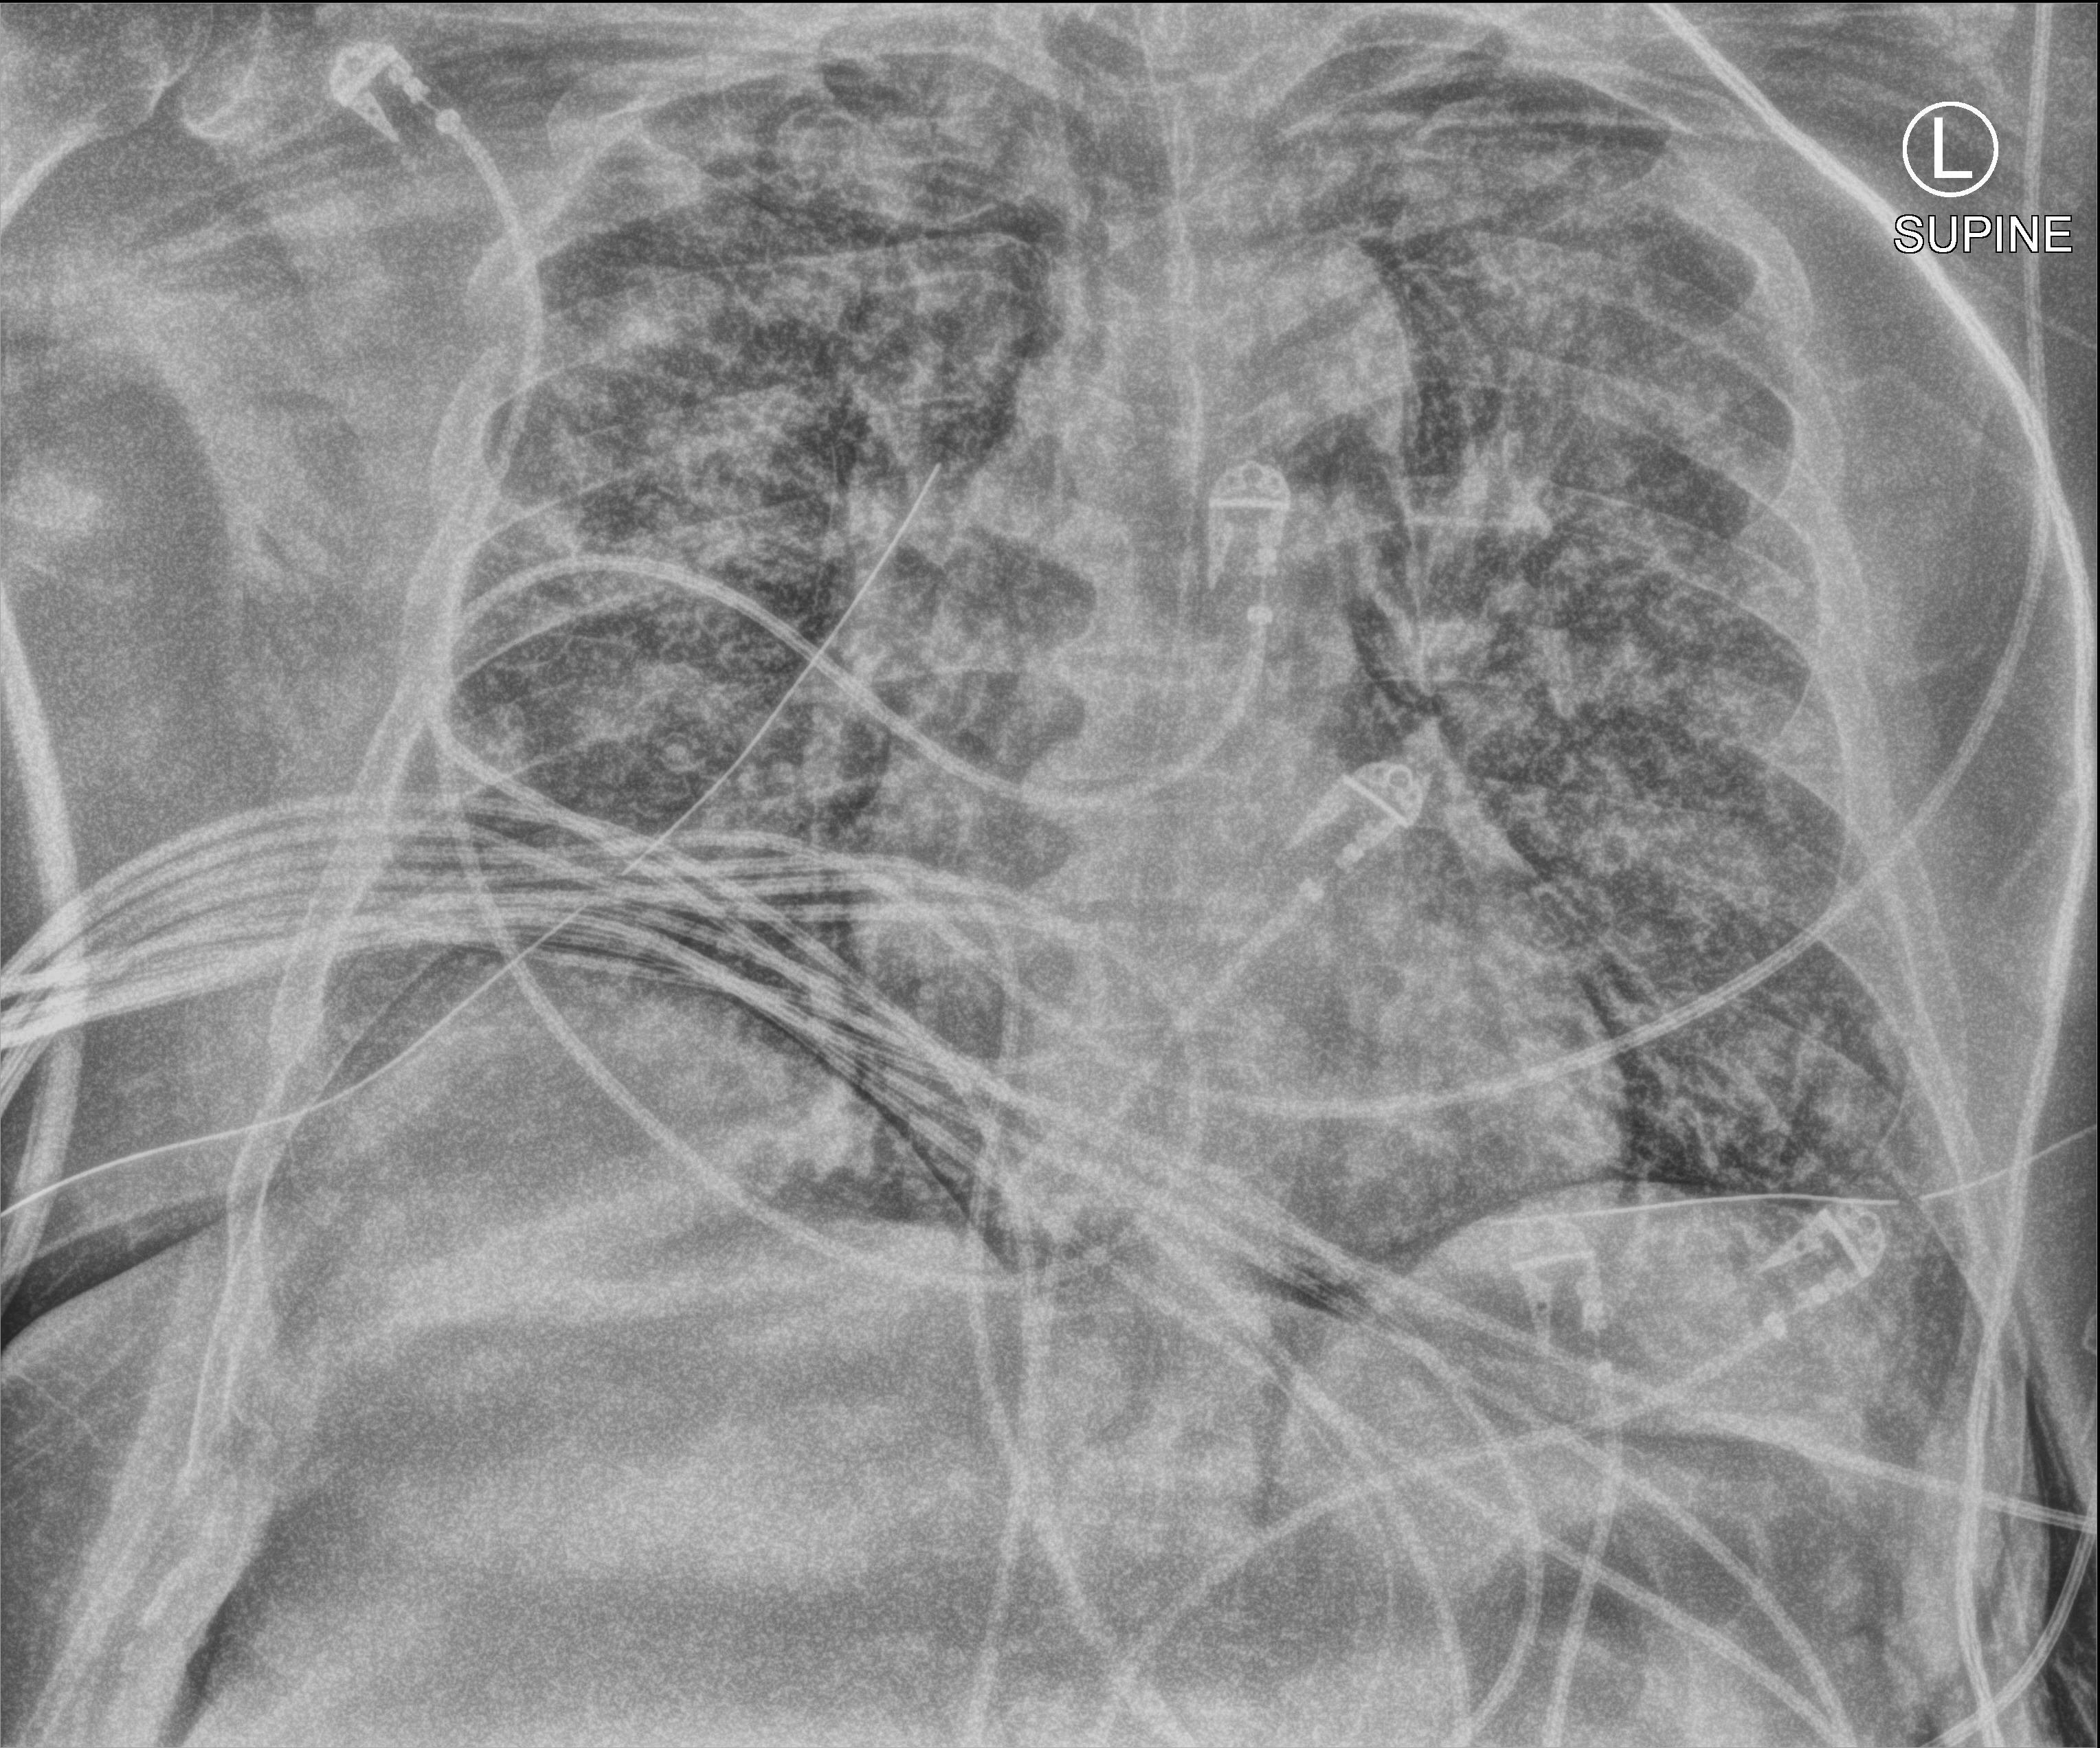
Bedside chest radiograph (computed radiography). Adult patient hospitalised with COVID-19, age 18–59 years.
From the hospital-stay record, not from the radiograph (when in the stay this image was taken is not recorded): length of hospital stay: 28 days; admitted to intensive care during this hospital stay: yes.